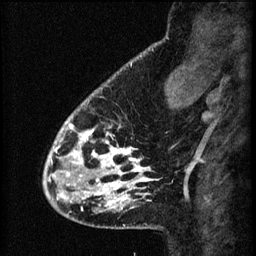
Breast MRI (dynamic contrast-enhanced), one sagittal slice. Slice 15 of 60 in the series (ordered by position). 3 images stored at this slice position (order not interpretable as contrast timing). 1.5 T. TE 4.2 ms, TR 8.2 ms. 2.2 mm slice thickness. 256 × 256 image matrix. Patient: female, 41 years.
Outlined on this slice (semi-automatically segmented with operator editing):
- analysis volume of interest (the breast-tissue region the enhancement analysis was run in; not a lesion): box from (x=56, y=104) to (x=157, y=207) px
- tumour enhancement mask (voxels above the 70 % enhancement threshold inside the analysis volume of interest): (x=56, y=116)–(x=157, y=207)